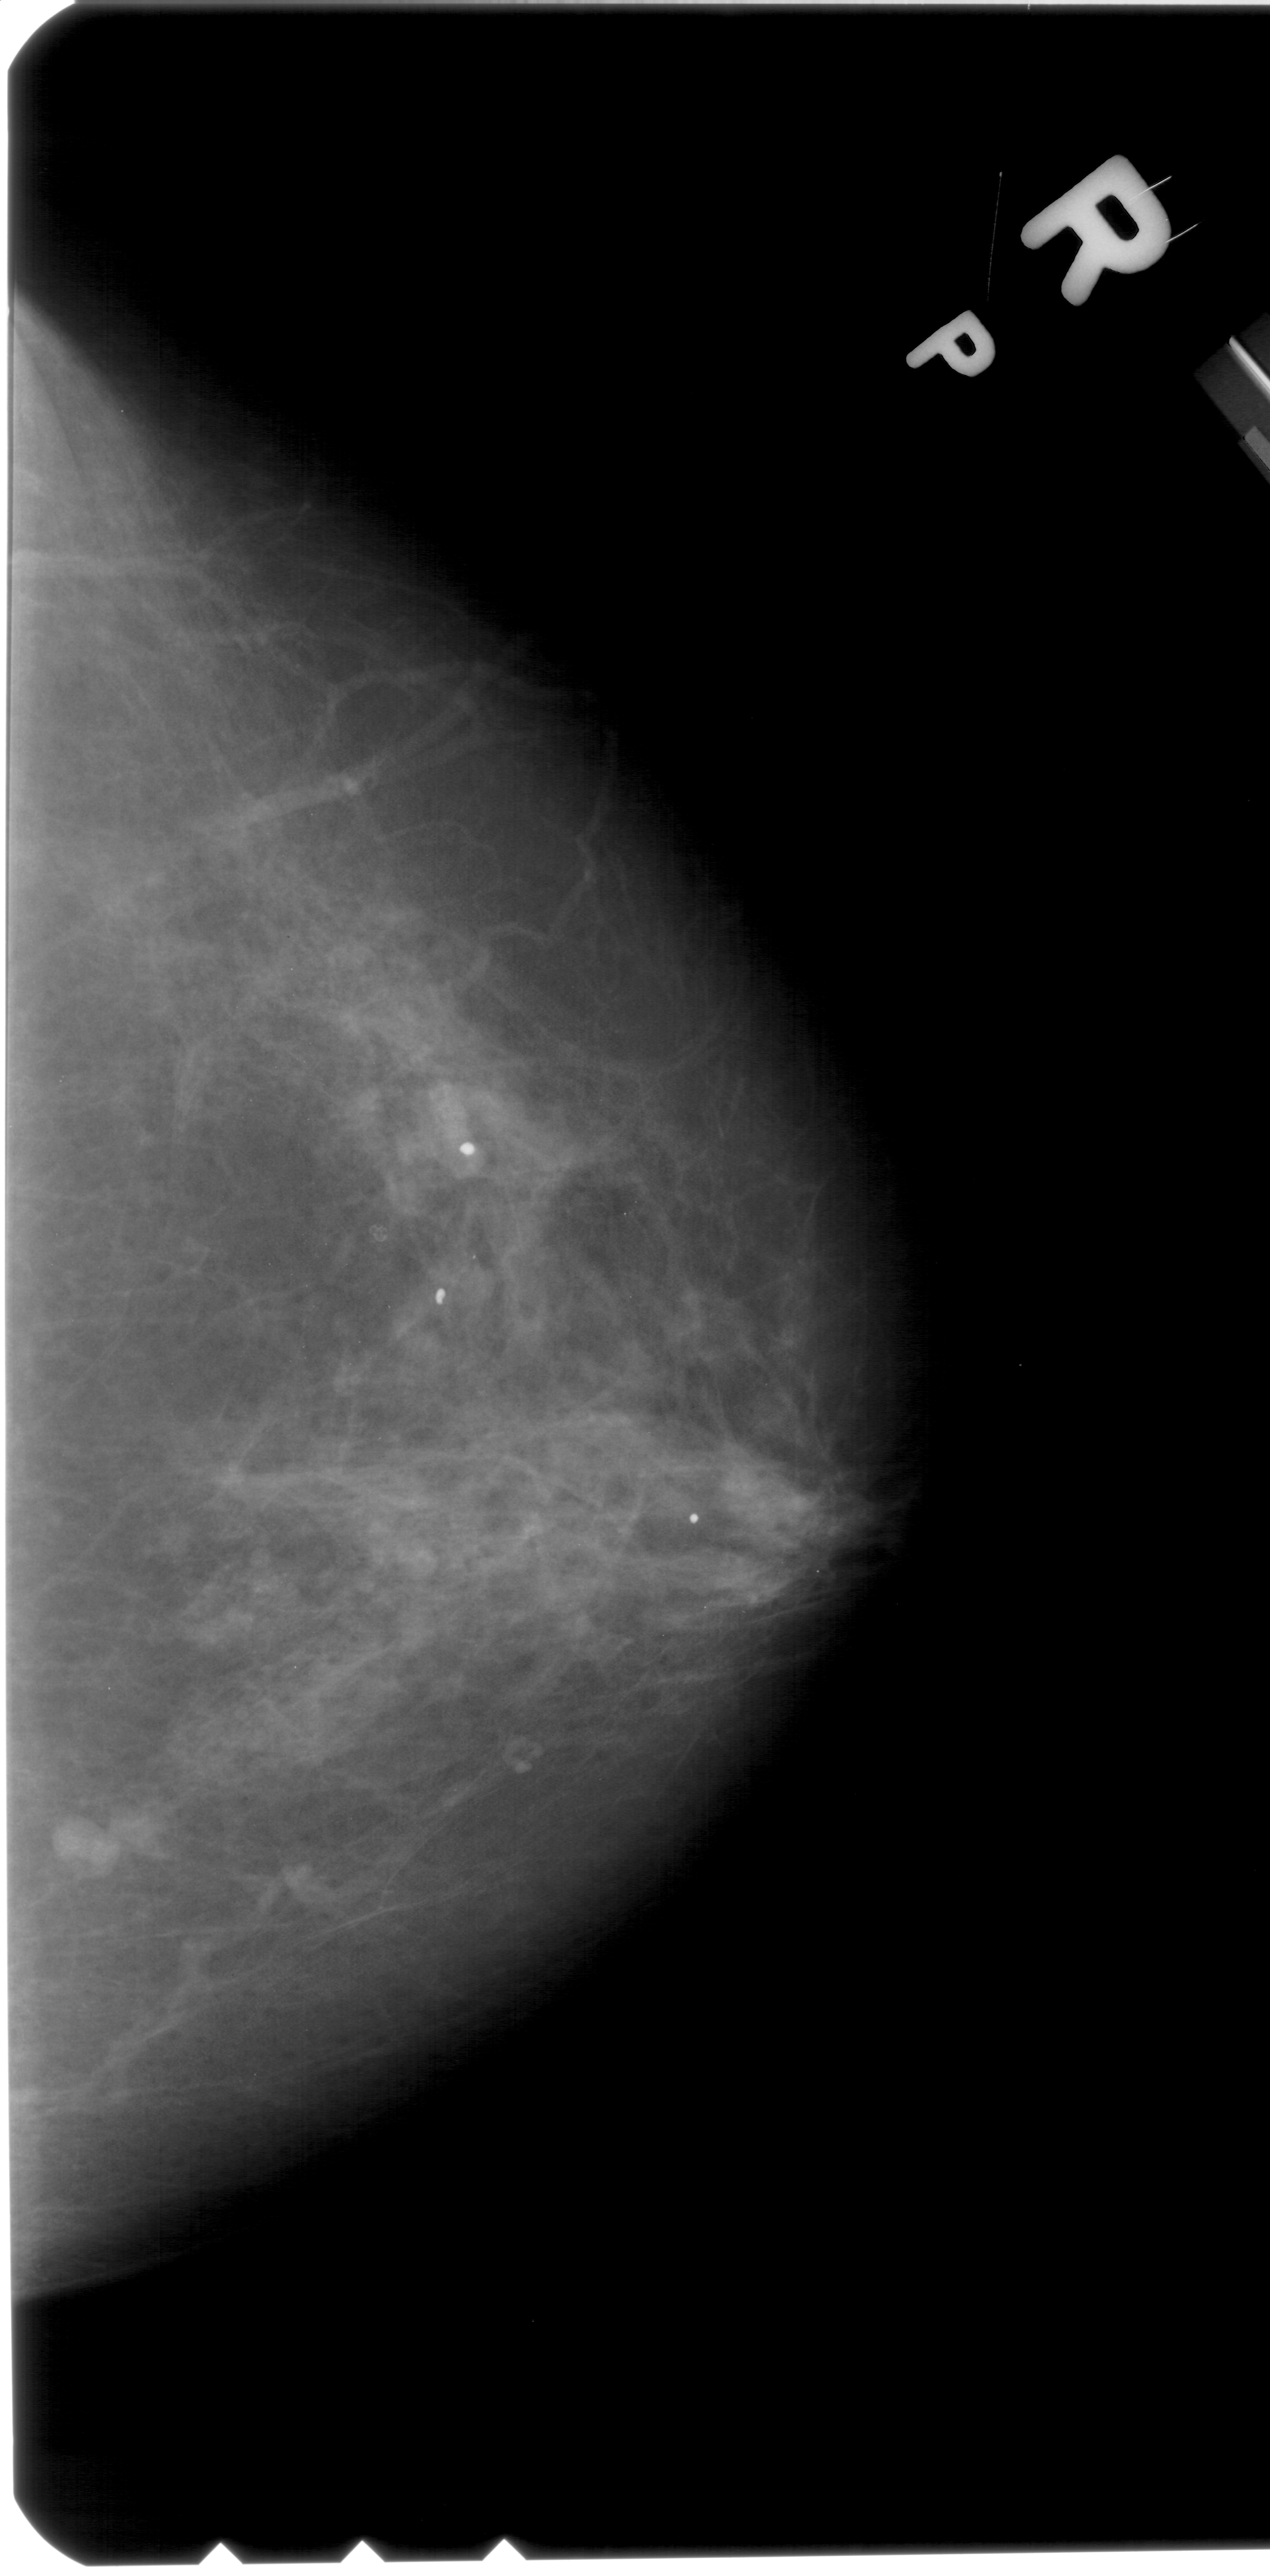
Digitized screen-film mammogram, right breast, CC view.
Marked abnormality: mass, shape lobulated, margins circumscribed; BI-RADS assessment category 4; subtlety rating 4 on a 1 (subtle) to 5 (obvious) scale; pathology result (as recorded, not read from the image): benign.